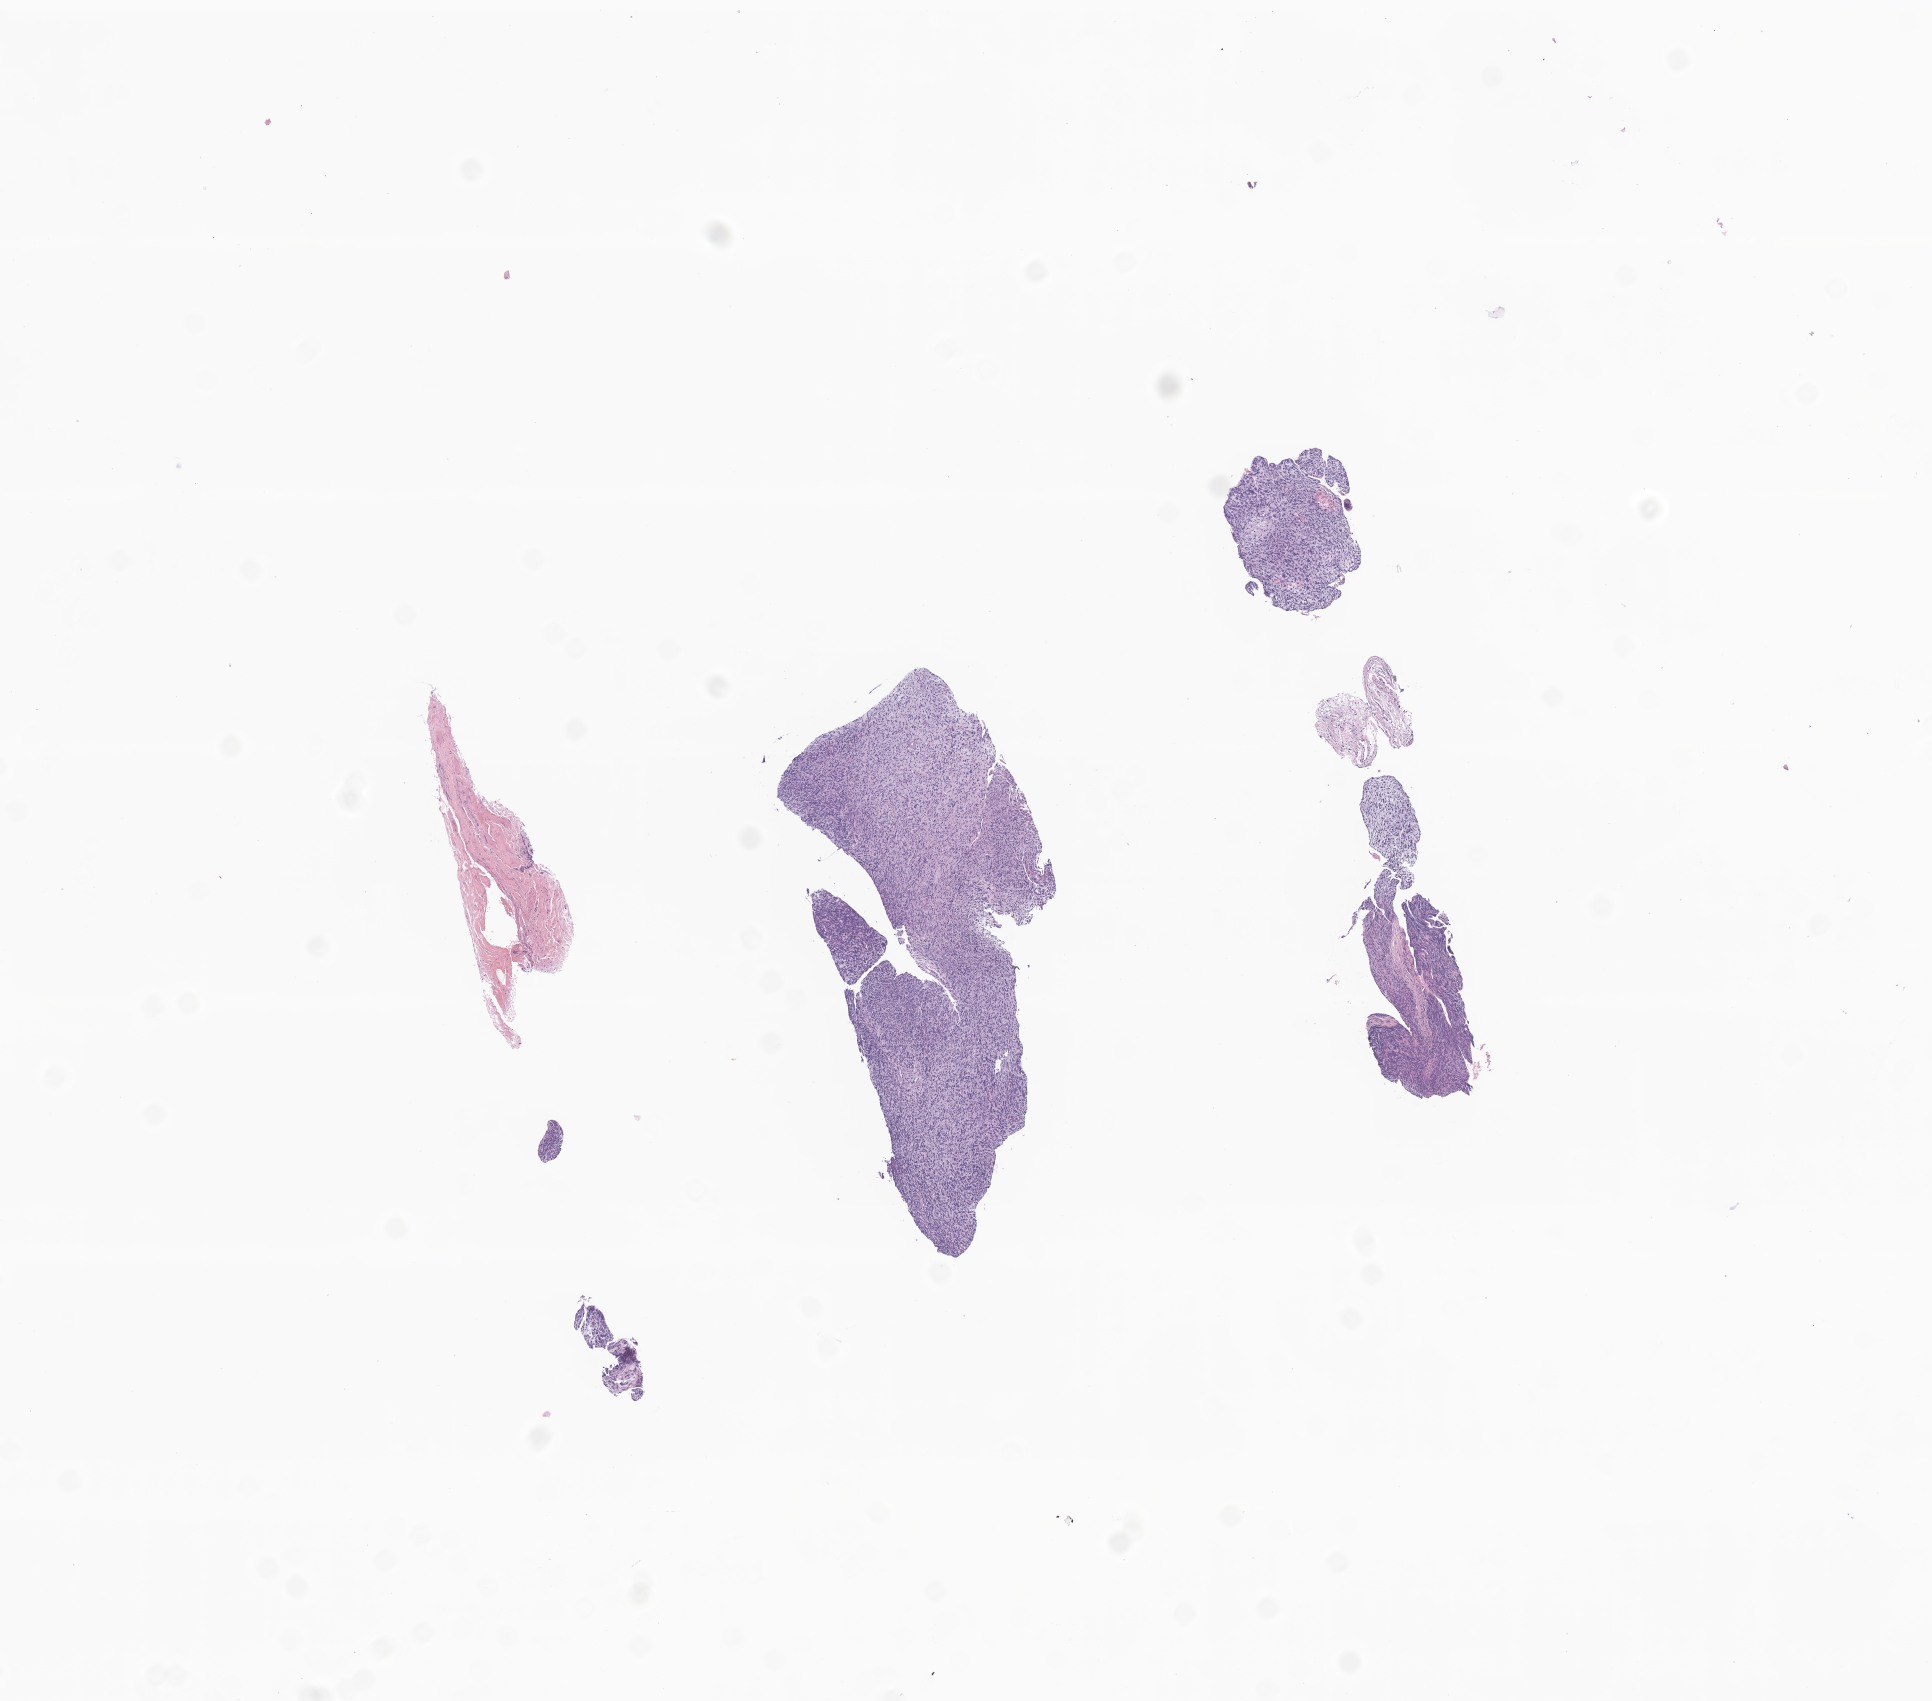
Haematoxylin and eosin whole-slide image of tumor tissue from the orbit, whole scanned area (about 8.1 x 7.2 mm) shown as a low-resolution overview, formalin-fixed, paraffin-embedded (FFPE) tissue. Patient: female, age 86 months (7 years 2 months).
Recorded diagnosis: Embryonal rhabdomyosarcoma, NOS.